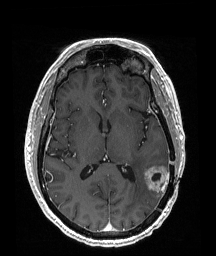
Brain MRI from a brain-tumour surgery series, one axial slice. Slice 91 of 192 in the series (ordered by position). T1-weighted post-contrast. 216 × 256 image matrix, field of view 211 × 250 mm. From the clinical record (not read from this slice): histopathology: Glioblastoma; WHO grade: 4; IDH mutation: no.
Annotated regions visible in this slice (outlined manually by an expert reader):
- tumour: bounding box [x1, y1, x2, y2] px = [144, 166, 170, 197]